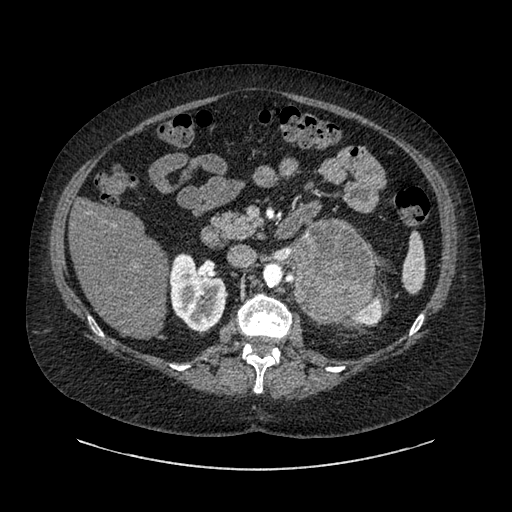
Contrast-enhanced abdominal CT, one axial slice; position 531 of 769 along the scan axis; reconstruction kernel SOFT; intravenous contrast given; soft-tissue window (W 400 / L 40 HU); 0.62 mm slice thickness; 512 × 512 image matrix. Patient: female, 61 years. From the clinical record (not read from this slice): diagnosis: adrenocortical carcinoma; tumour side: left adrenal; tumour size at pathology: 13 cm; Ki-67 index: 79 %; stage (as recorded): 2.
Outlined on this slice (semi-automatically segmented with operator editing):
- mass: bounding box (x1, y1, x2, y2) in pixels: (293, 221, 374, 321)